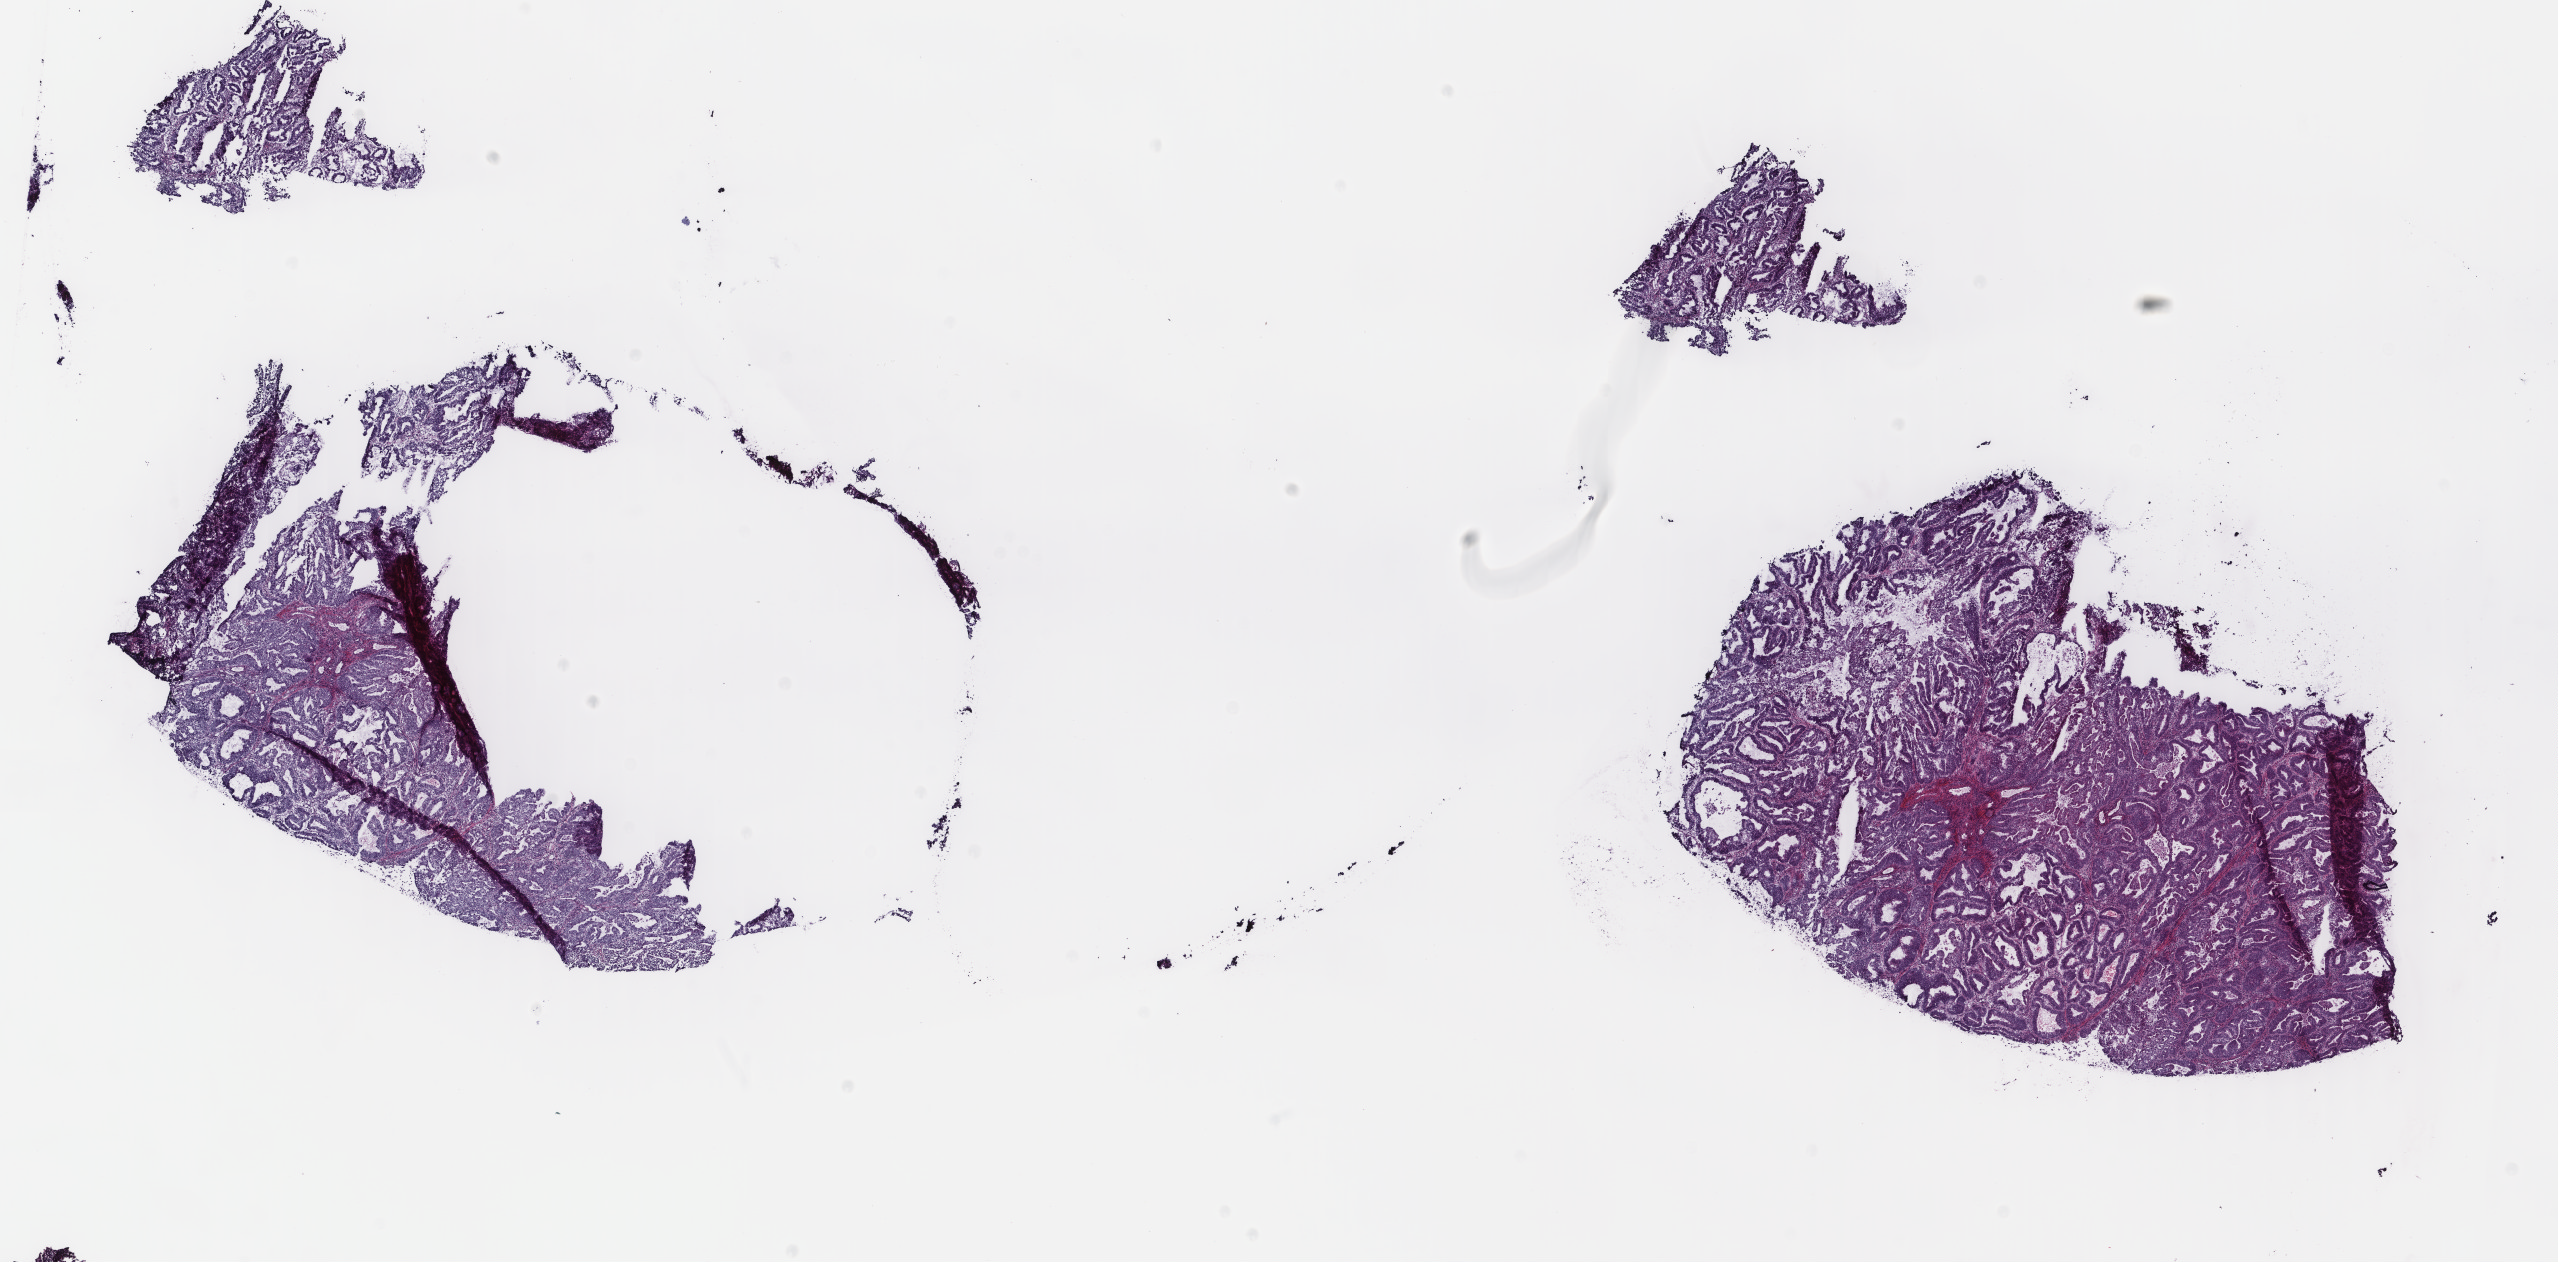
Digitized H&E-stained tissue section (whole slide), whole scanned area (about 20.3 x 10.0 mm) shown as a low-resolution overview. Frozen section from the top of the tissue portion. Sample: primary tumour, uterus. Patient: female, age at initial diagnosis 70 years. Histologic grade: G2 (moderately differentiated). Slide review estimates, as recorded: tumour cells 100%, tumour nuclei 75%, normal cells 0%, stromal cells 0%, necrosis 0%. Inflammatory infiltration, as recorded: lymphocyte infiltration 0%, monocyte infiltration 0%, neutrophil infiltration 0%.
* pathologic diagnosis: Endometrioid adenocarcinoma, NOS (endometrium)
* FIGO stage: IA